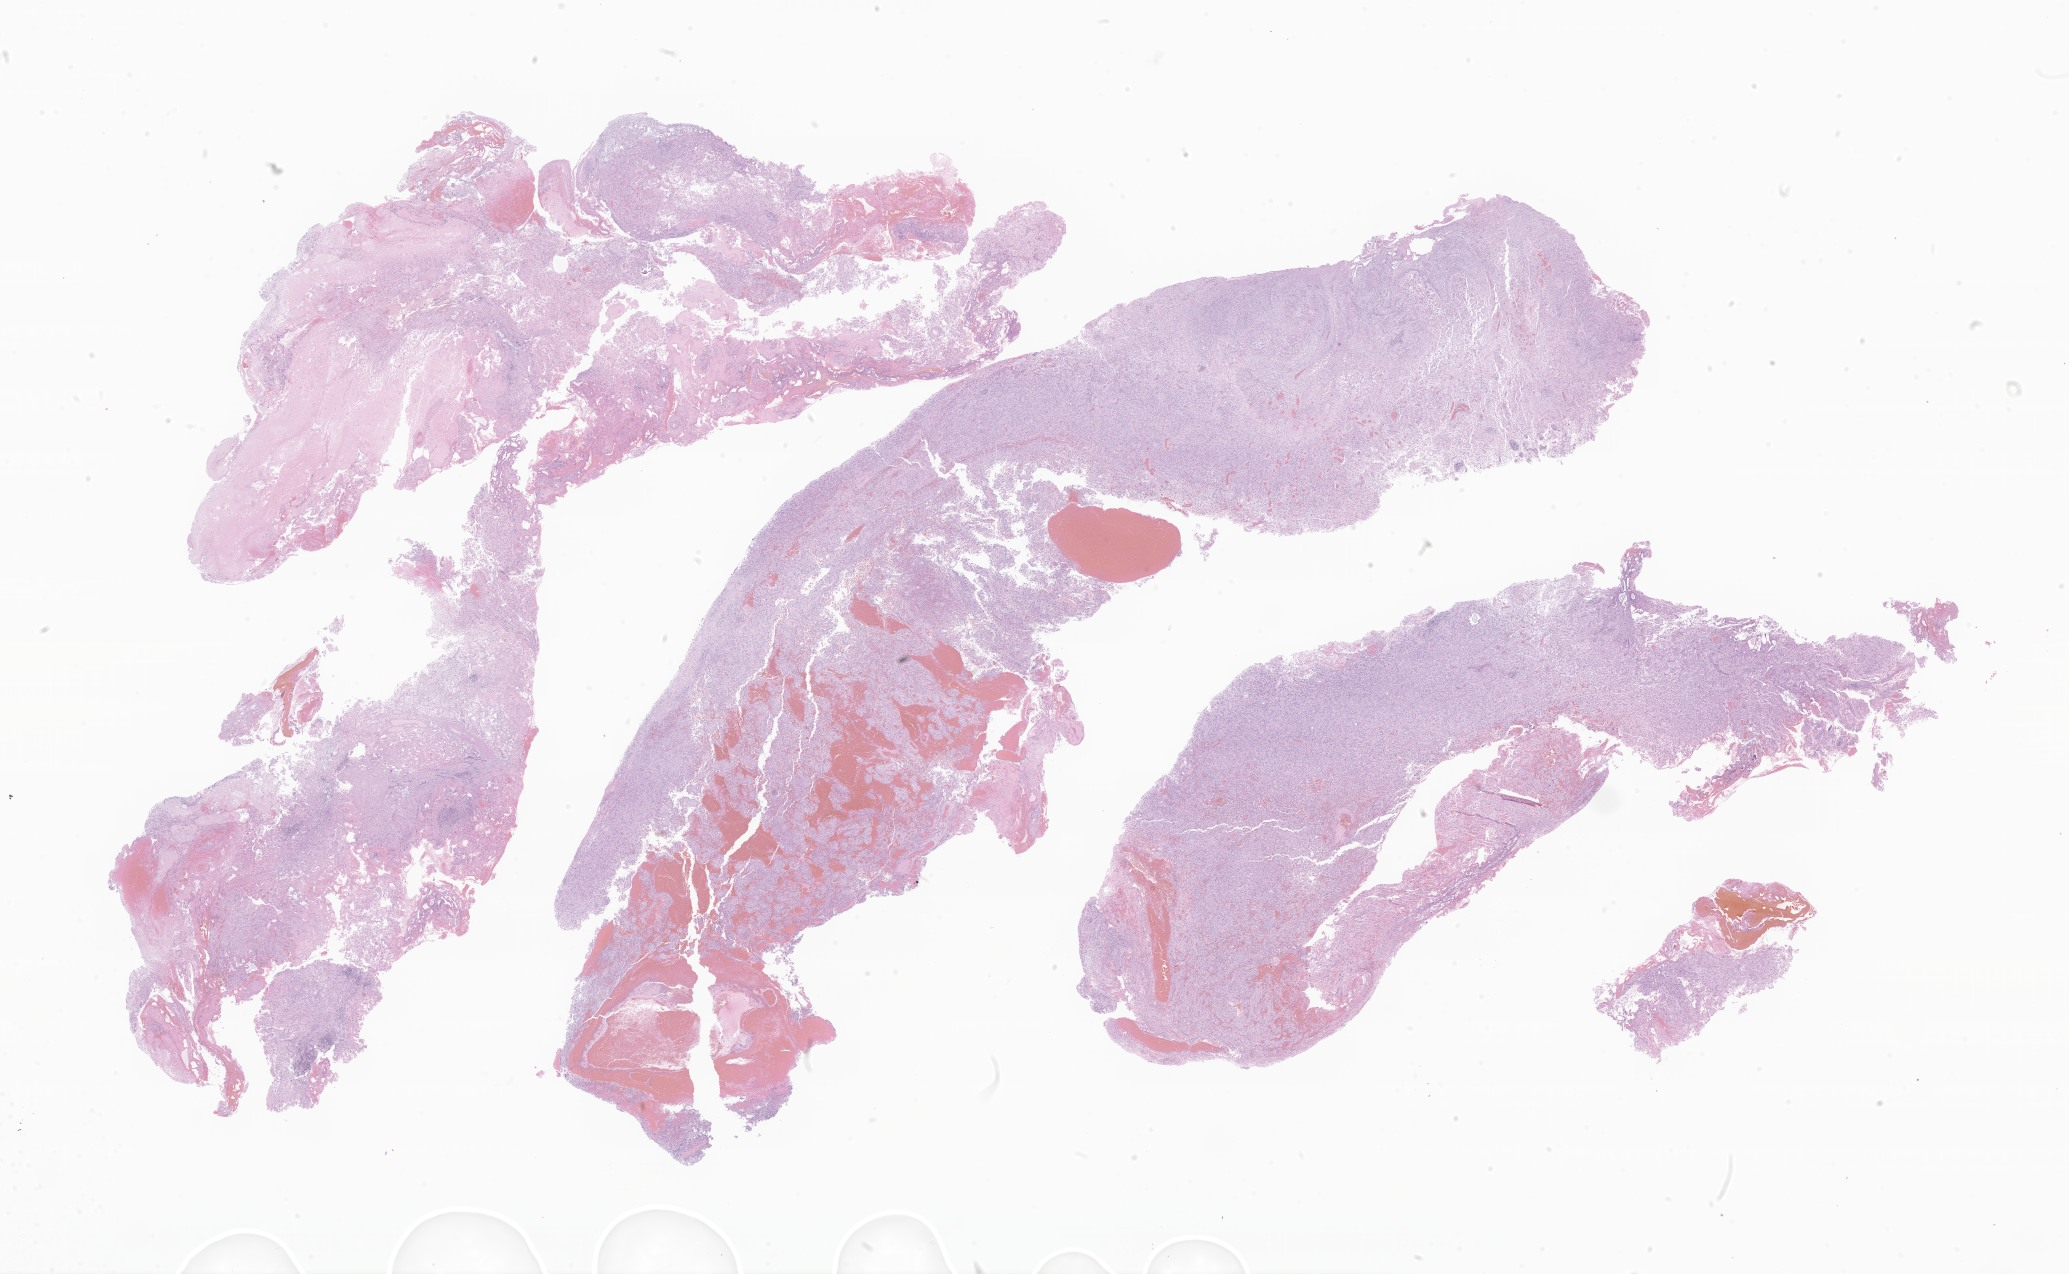
Hematoxylin and eosin (H&E) whole-slide image of tumor tissue from the brain, shown as a low-resolution overview of the whole scanned area (about 34.9 x 21.5 mm), formalin-fixed, paraffin-embedded (FFPE) tissue. Patient: female, age 178 months (14 years 10 months).
Diagnosis: Neoplasm, malignant.